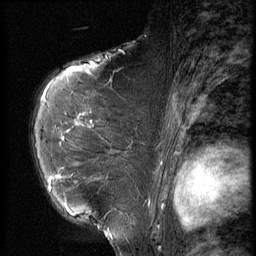
Breast MRI (dynamic contrast-enhanced), one sagittal slice; position 42 of 56 along the scan axis; 3 images stored at this slice position (order not interpretable as contrast timing); 1.5 T; TE 4.2 ms, TR 9 ms; 2.5 mm slice thickness; 256 × 256 image matrix, field of view 180 × 180 mm. Female patient, age 61 years. From the clinical record (not read from this slice): setting: breast cancer imaged before/during neoadjuvant chemotherapy; receptor status: HR-positive, HER2-negative.
Outlined on this slice (semi-automatic segmentation, software-assisted and operator-edited):
- analysis volume of interest (the breast-tissue region the enhancement analysis was run in; not a lesion): bounding box [x1, y1, x2, y2] px = [47, 89, 153, 191]
- tumour enhancement mask (voxels above the 140 % enhancement threshold inside the analysis volume of interest): [49, 123, 80, 189]